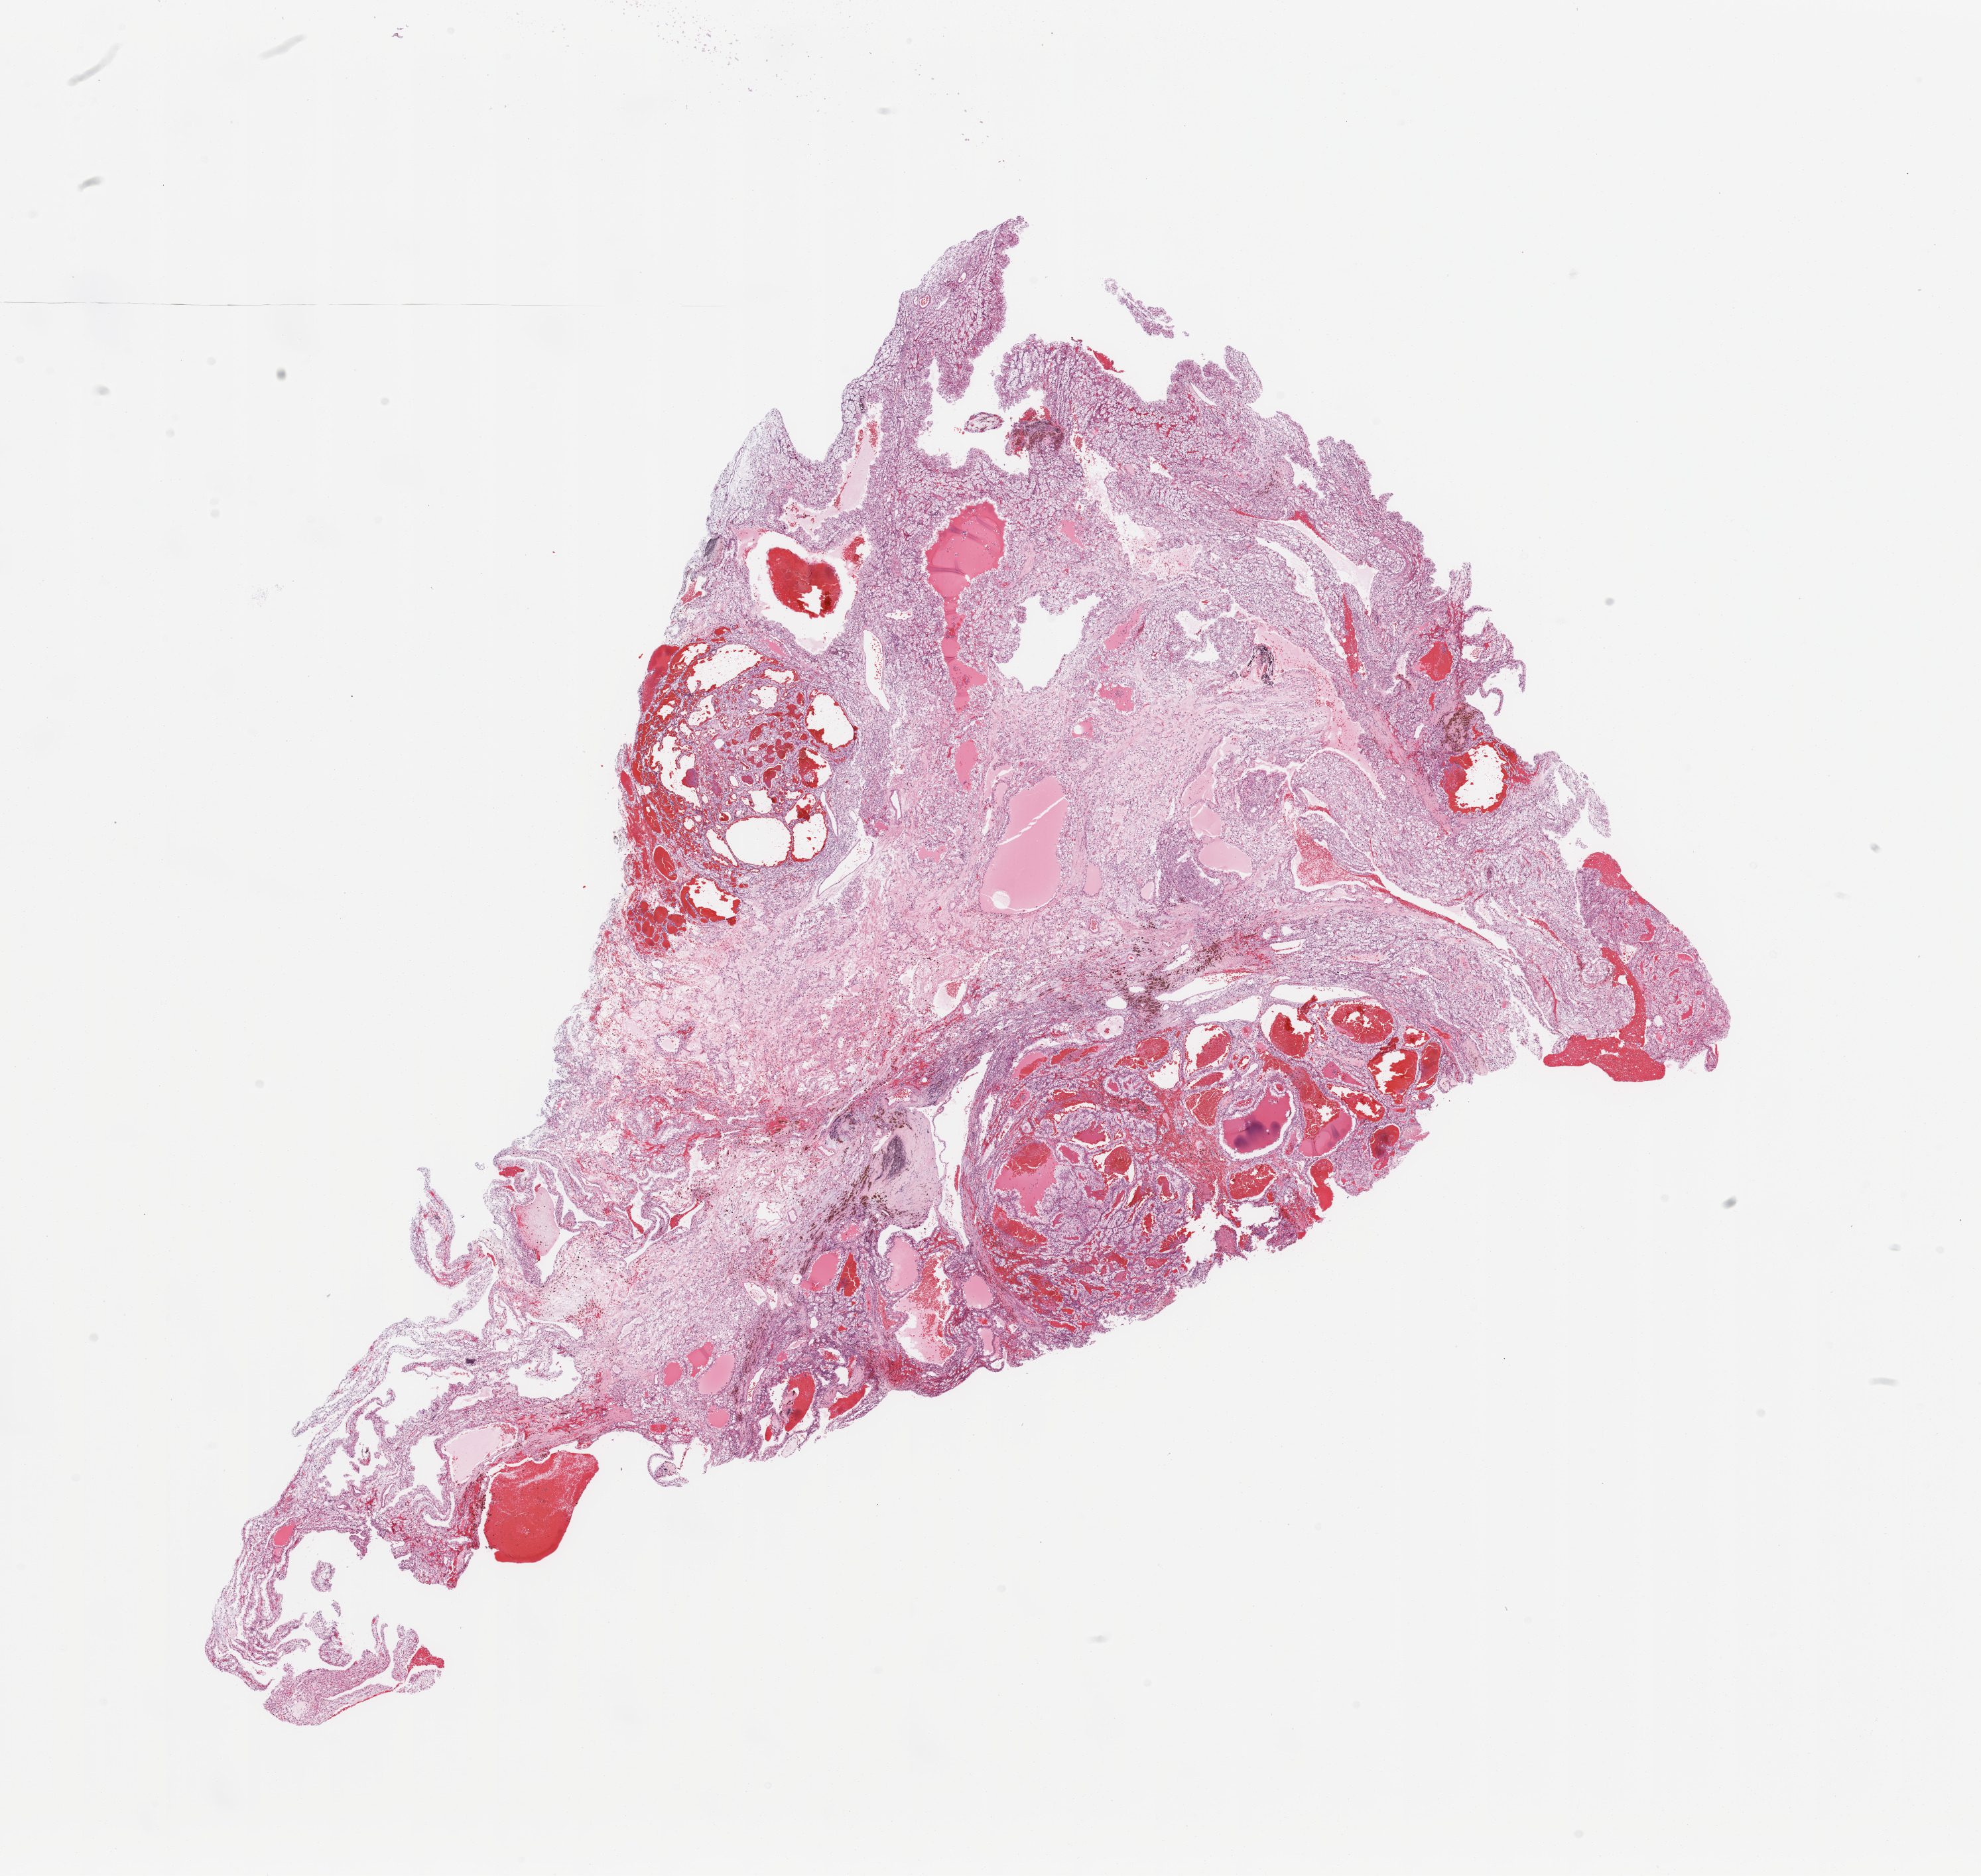
Whole-slide histology image, Hematoxylin and eosin (H&E) stained, shown as a low-resolution overview of the whole scanned area (about 23.6 x 22.4 mm), tumour tissue sample, sampled site: kidney. 55-year-old male patient. Histologic grade: G2 (moderately differentiated). Composition of this section per pathologist review: tumour nuclei 80%, necrosis 5%.
Histologic diagnosis: Renal cell carcinoma, NOS. AJCC pathologic stage: I. Primary tumour site (as recorded): lower pole.